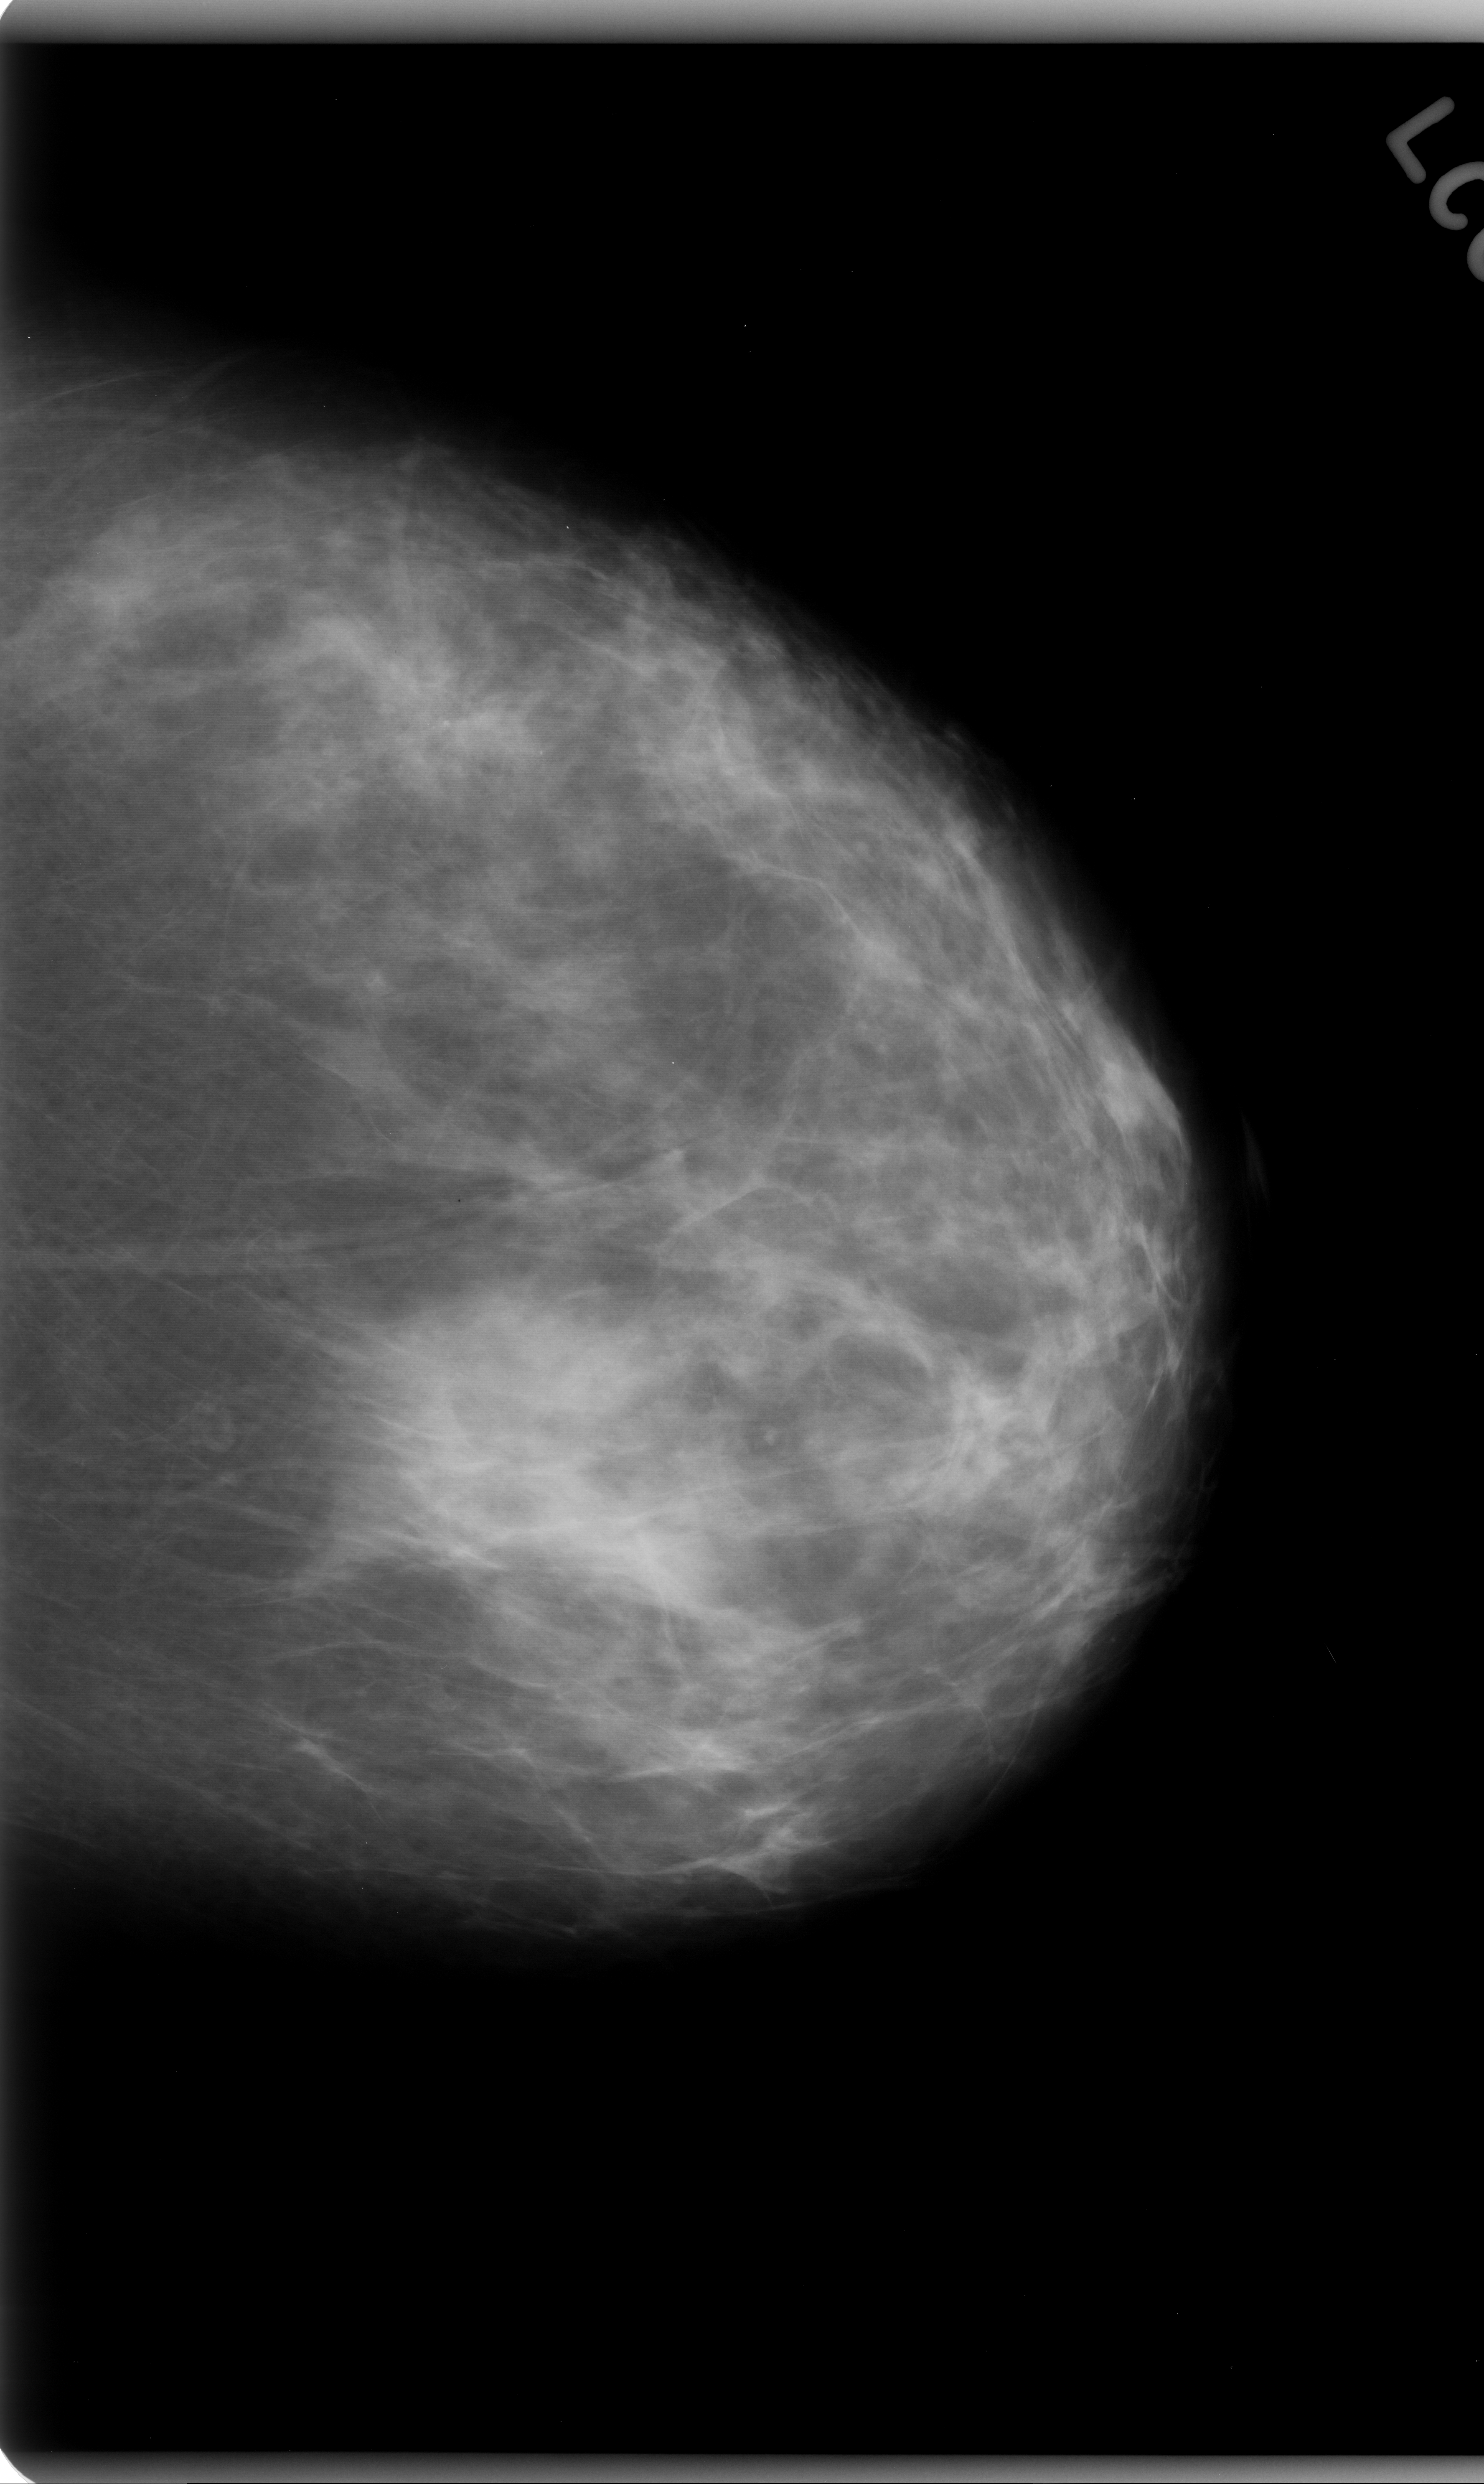
Scanned film-screen mammogram, left breast, CC view, BI-RADS breast density category 2 (scale 1–4).
Finding: calcifications, morphology pleomorphic, distribution clustered; BI-RADS assessment category 4; pathology (as recorded): malignant.